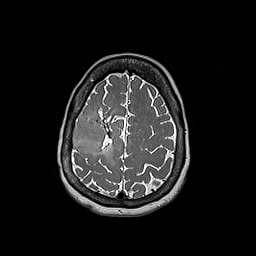
Brain MRI from a brain-tumour surgery series, one axial slice; slice 55 of 192 in the series (ordered by position); 1 mm slice thickness; 256 × 256 image matrix. From the clinical record (not read from this slice): histopathology: Oligodendroglioma; WHO grade: 3; IDH mutation: yes; tumour location: Right Frontal.
Structures marked on this image (expert manual segmentation):
- tumour: bounding box <72,113,105,153> (left, top, right, bottom; pixels)